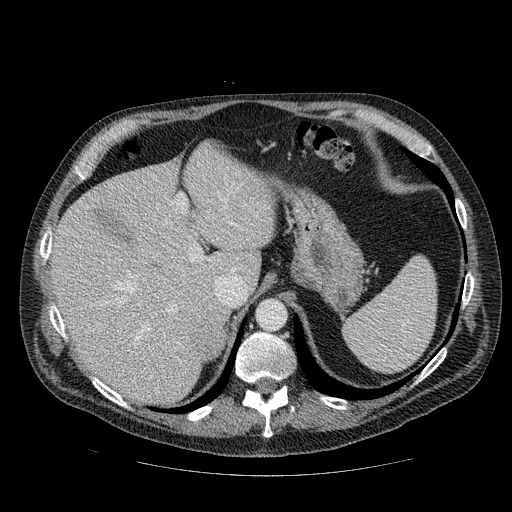
Contrast-enhanced abdominal CT, one axial slice. Position 71 of 111 along the scan axis. Reconstruction kernel STANDARD. 120 kVp. Intravenous contrast given. Soft-tissue window (W 400 / L 40 HU). 512 × 512 image matrix. Male patient, age 56 years. Case-level facts recorded for this patient, not image findings: diagnosis: adrenocortical carcinoma; tumour side: right adrenal; tumour size at pathology: 9 cm; Ki-67 index: 48 %; stage (as recorded): 4.
Outlined on this slice (semi-automatically segmented with operator editing):
- mass: bounding box [x1, y1, x2, y2] px = [194, 326, 224, 359]